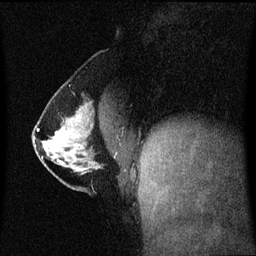
Breast MRI (dynamic contrast-enhanced), one sagittal slice; position 26 of 60 along the scan axis; dynamic contrast-enhanced series, image 2 of 3 at this slice position (ordered by acquisition); 1.5 T; TE 4.2 ms, TR 8.4 ms; 256 × 256 image matrix, field of view 210 × 210 mm. Female patient, age 40 years. Case-level facts recorded for this patient, not image findings: setting: breast cancer imaged before/during neoadjuvant chemotherapy; receptor status: triple-negative.
Outlined on this slice (semi-automatic segmentation, software-assisted and operator-edited):
- analysis volume of interest (the breast-tissue region the enhancement analysis was run in; not a lesion): bounding box <33,112,107,188> (left, top, right, bottom; pixels)
- tumour enhancement mask (voxels above the 70 % enhancement threshold inside the analysis volume of interest): <38,130,65,151>